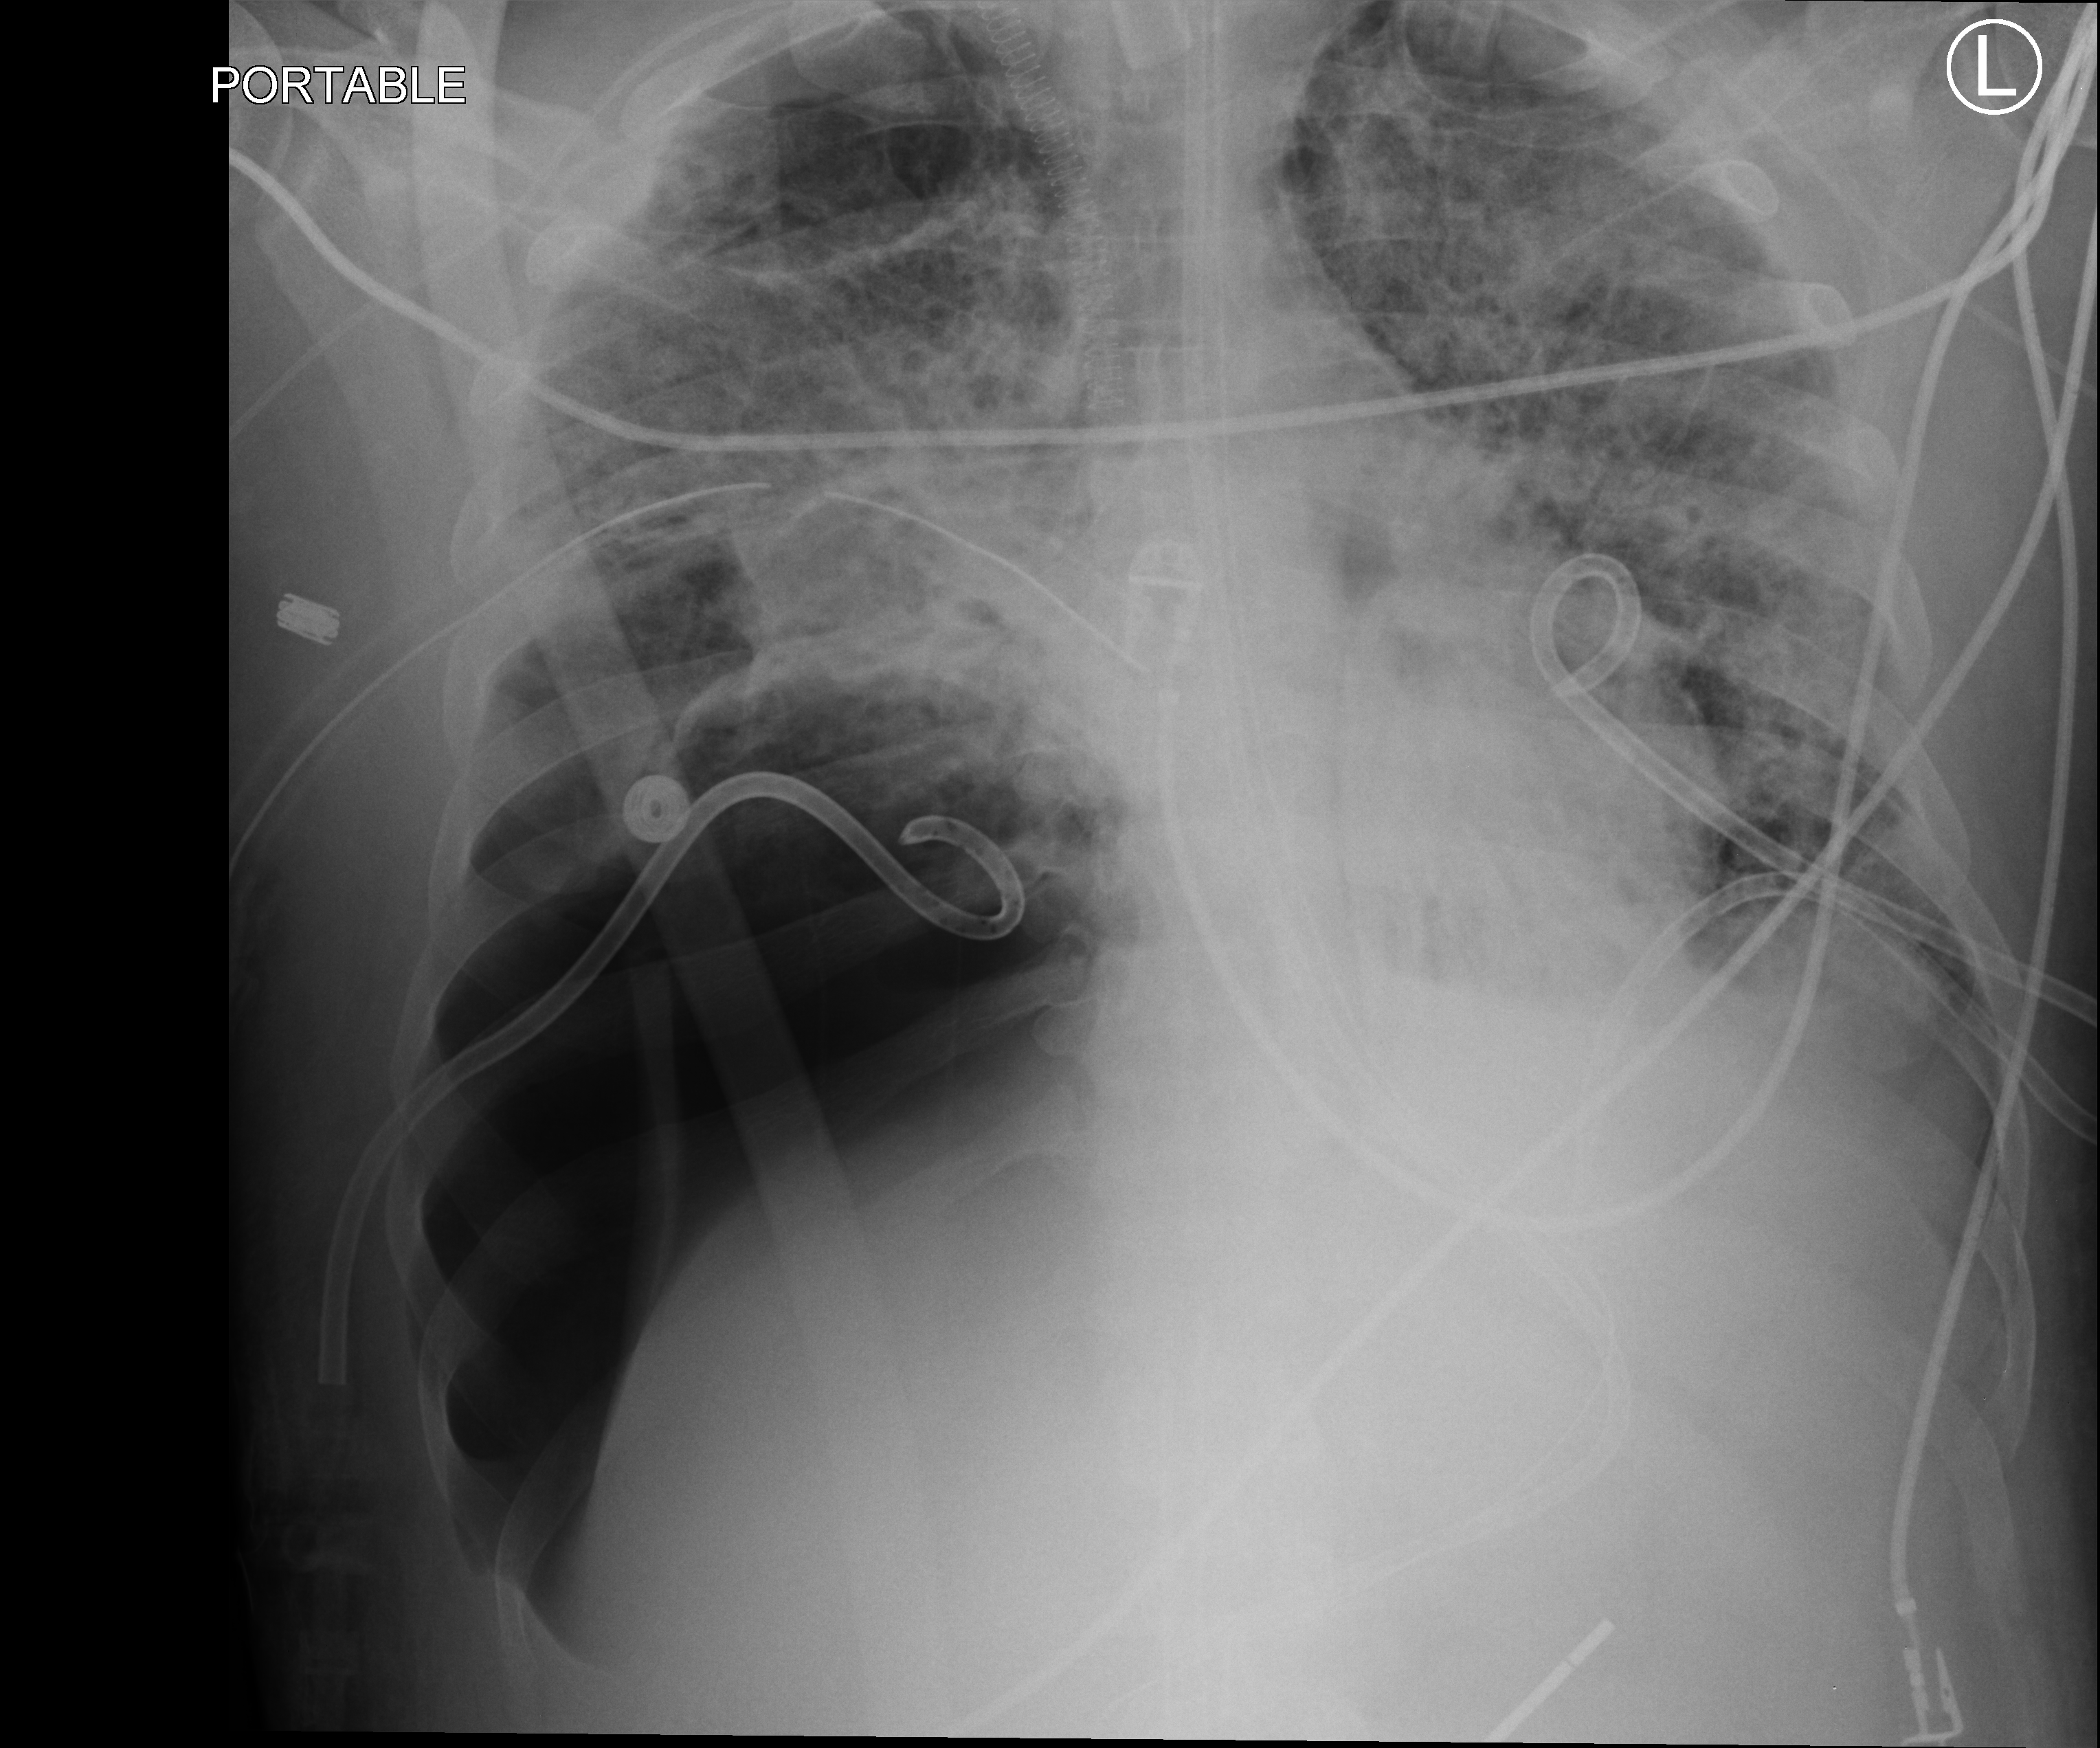
Portable chest radiograph; anteroposterior (AP) projection. Adult patient hospitalised with COVID-19, age 18–59 years.
Hospital-stay facts (about this admission, not read from this image; timing relative to this image not recorded): length of hospital stay: 60 days; chronic kidney disease (admission record): no.